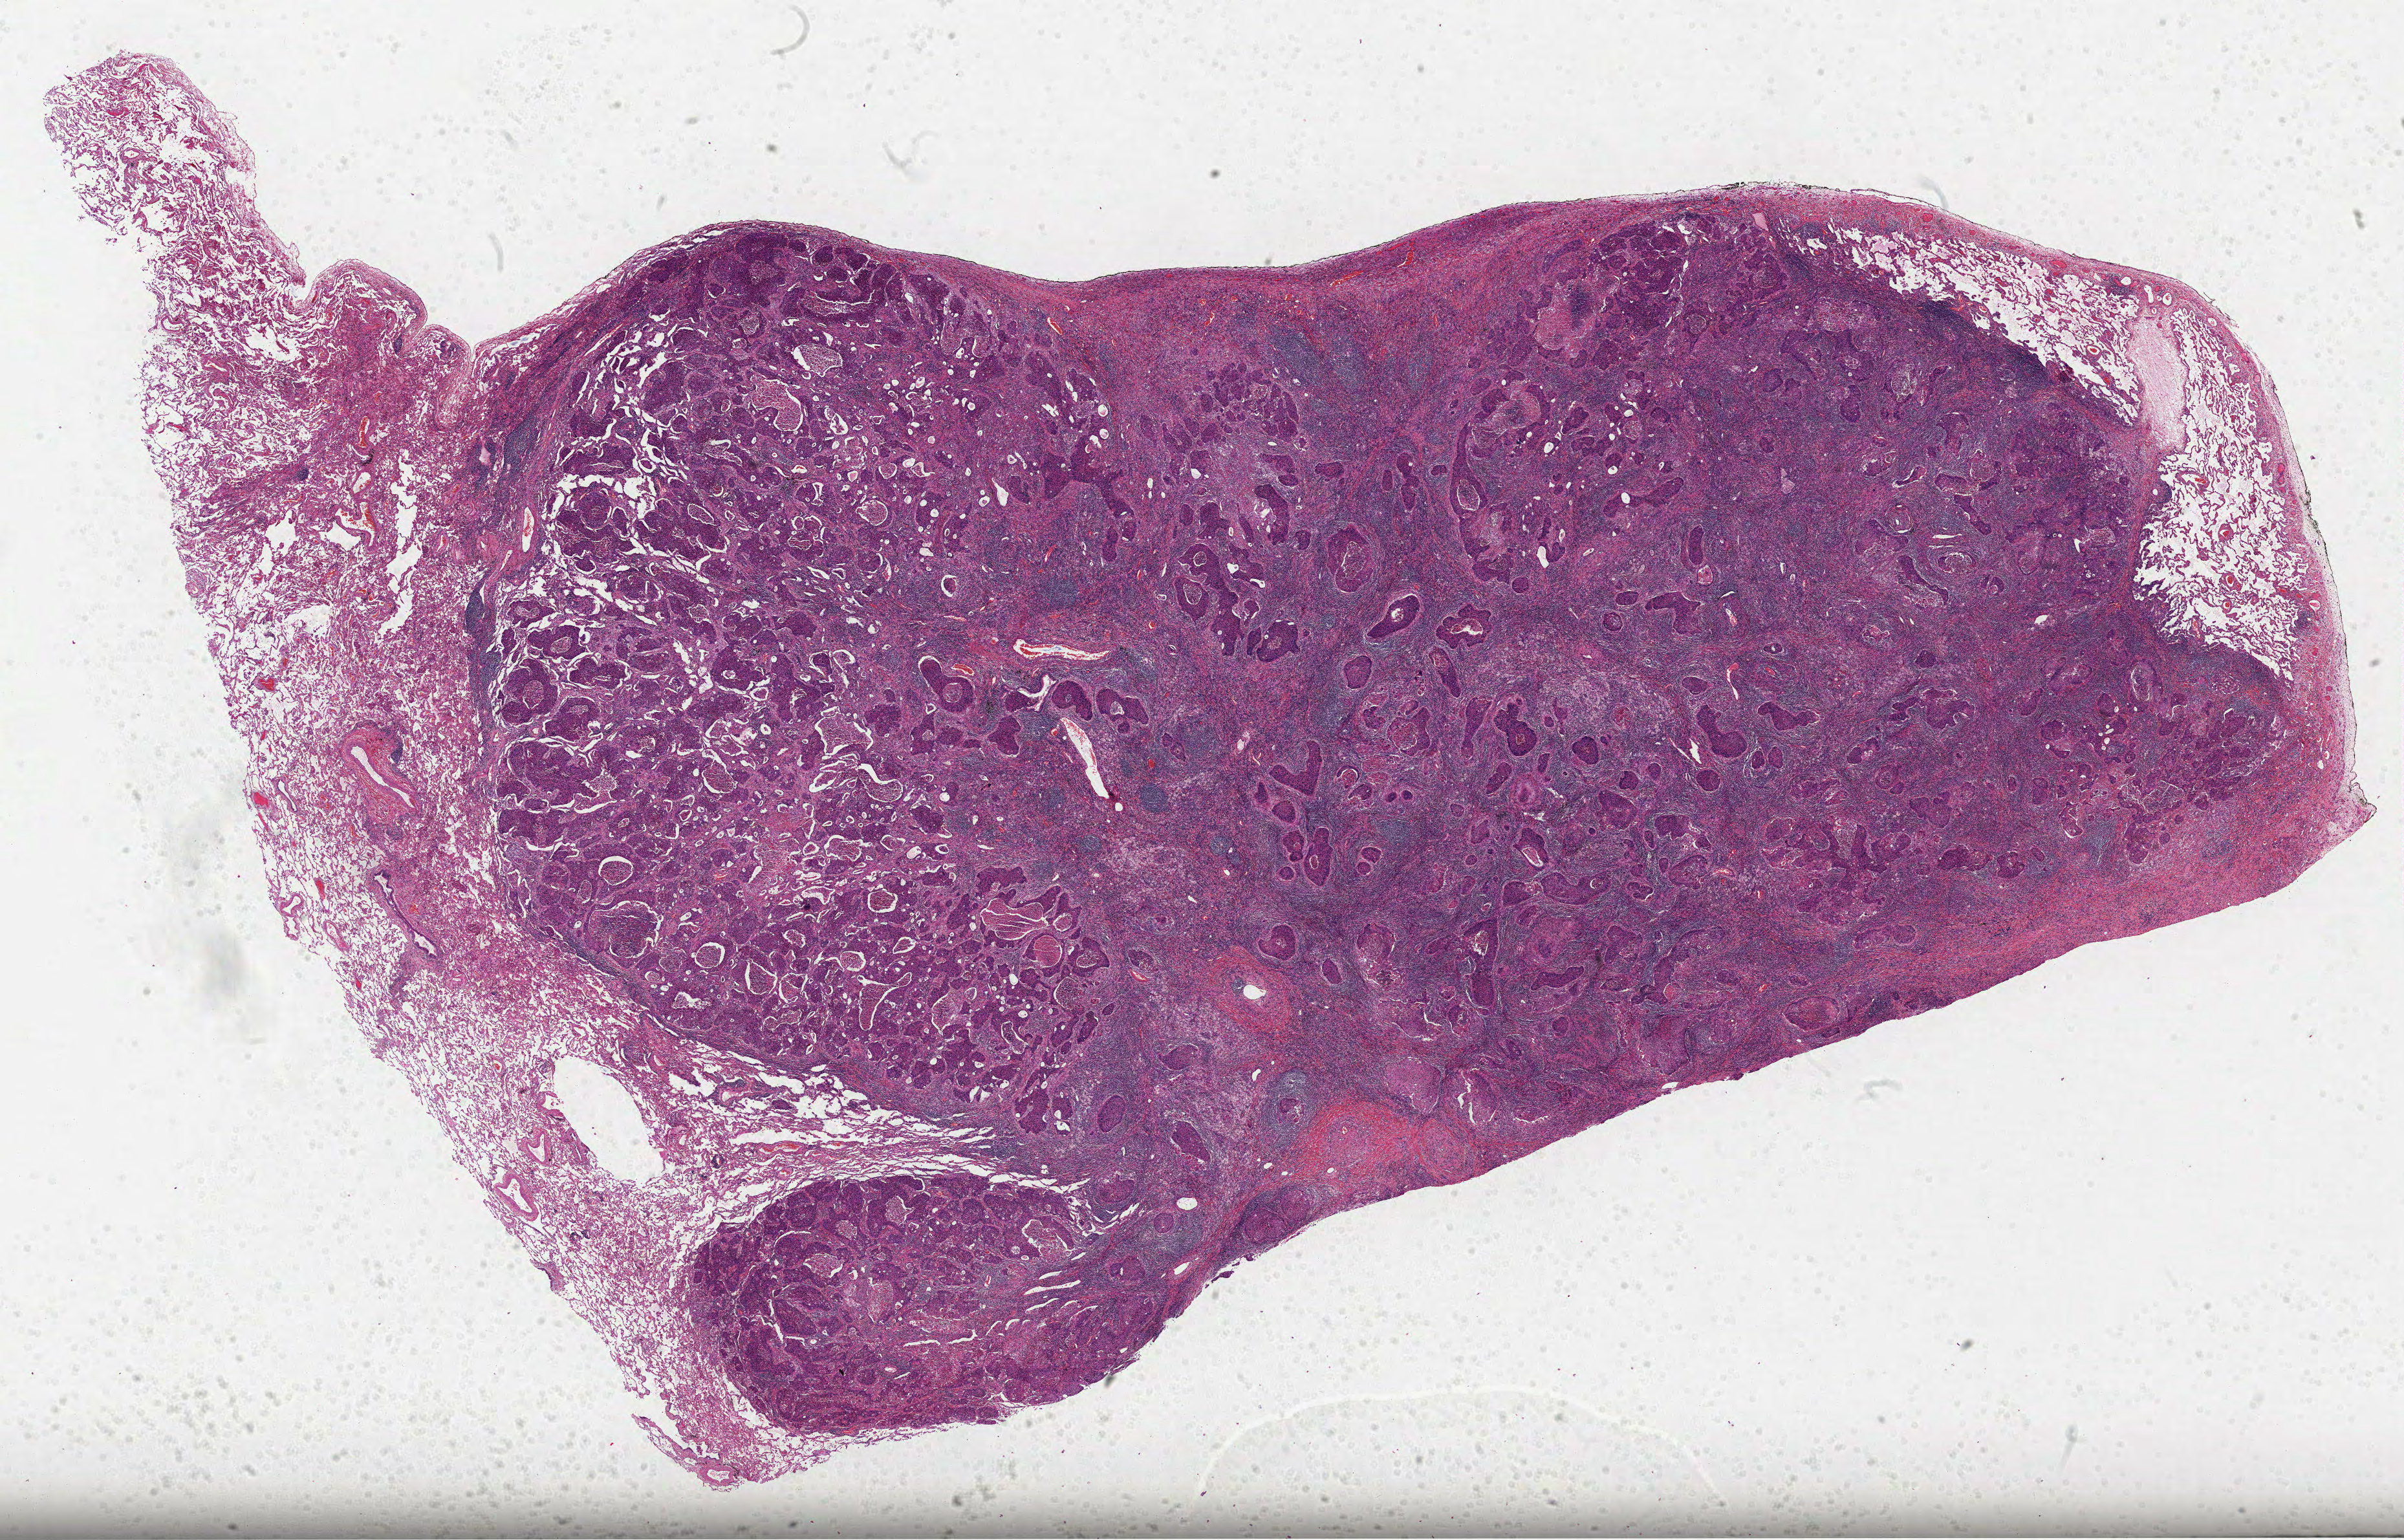
Digitized H&E tissue section (whole slide) — a low-resolution overview of the entire scanned area, about 30.0 x 19.2 mm. FFPE section. Primary tumour sample from the lung. Patient: male, age at initial diagnosis 75 years.
* AJCC pathologic stage: IB (6th edition)
* diagnosis: Squamous cell carcinoma, NOS (upper lobe, lung)